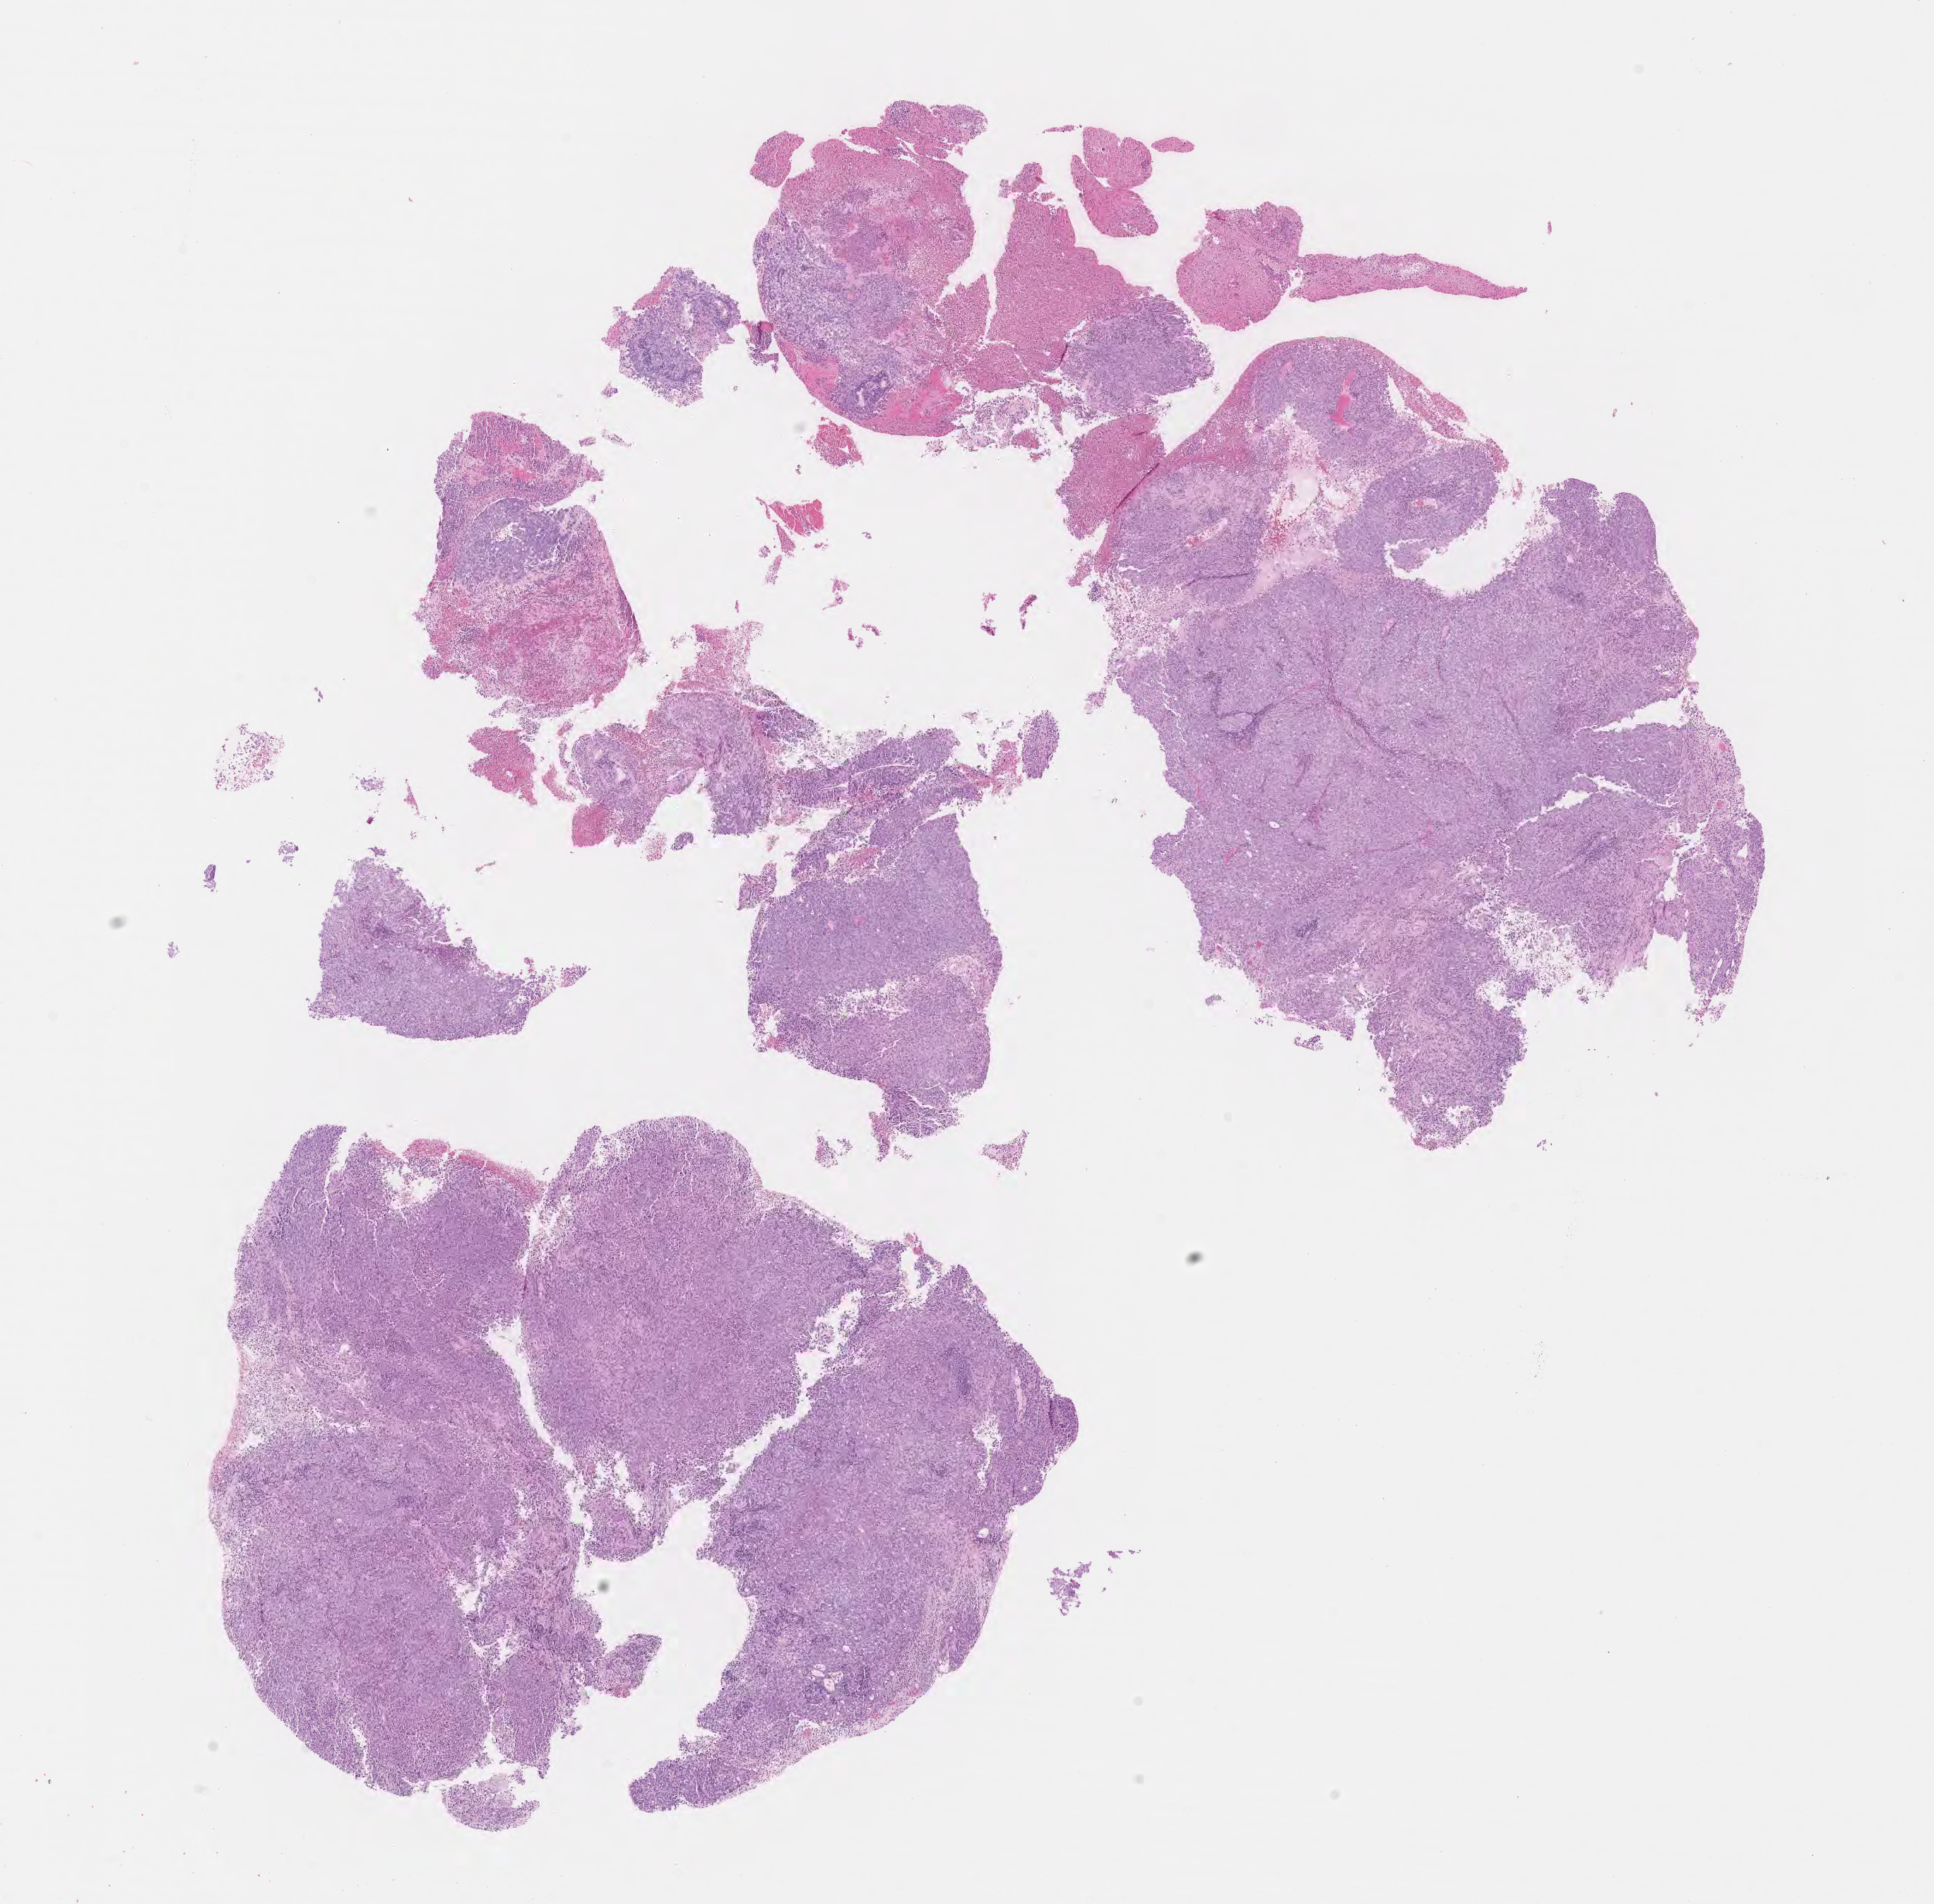
H&E whole-slide image — whole scanned area (about 11.1 x 10.9 mm) shown as a low-resolution overview. Tumor tissue. Anatomic site: cervix. Female patient, 70 years old.
• diagnosis: Squamous cell carcinoma, large cell, nonkeratinizing, NOS